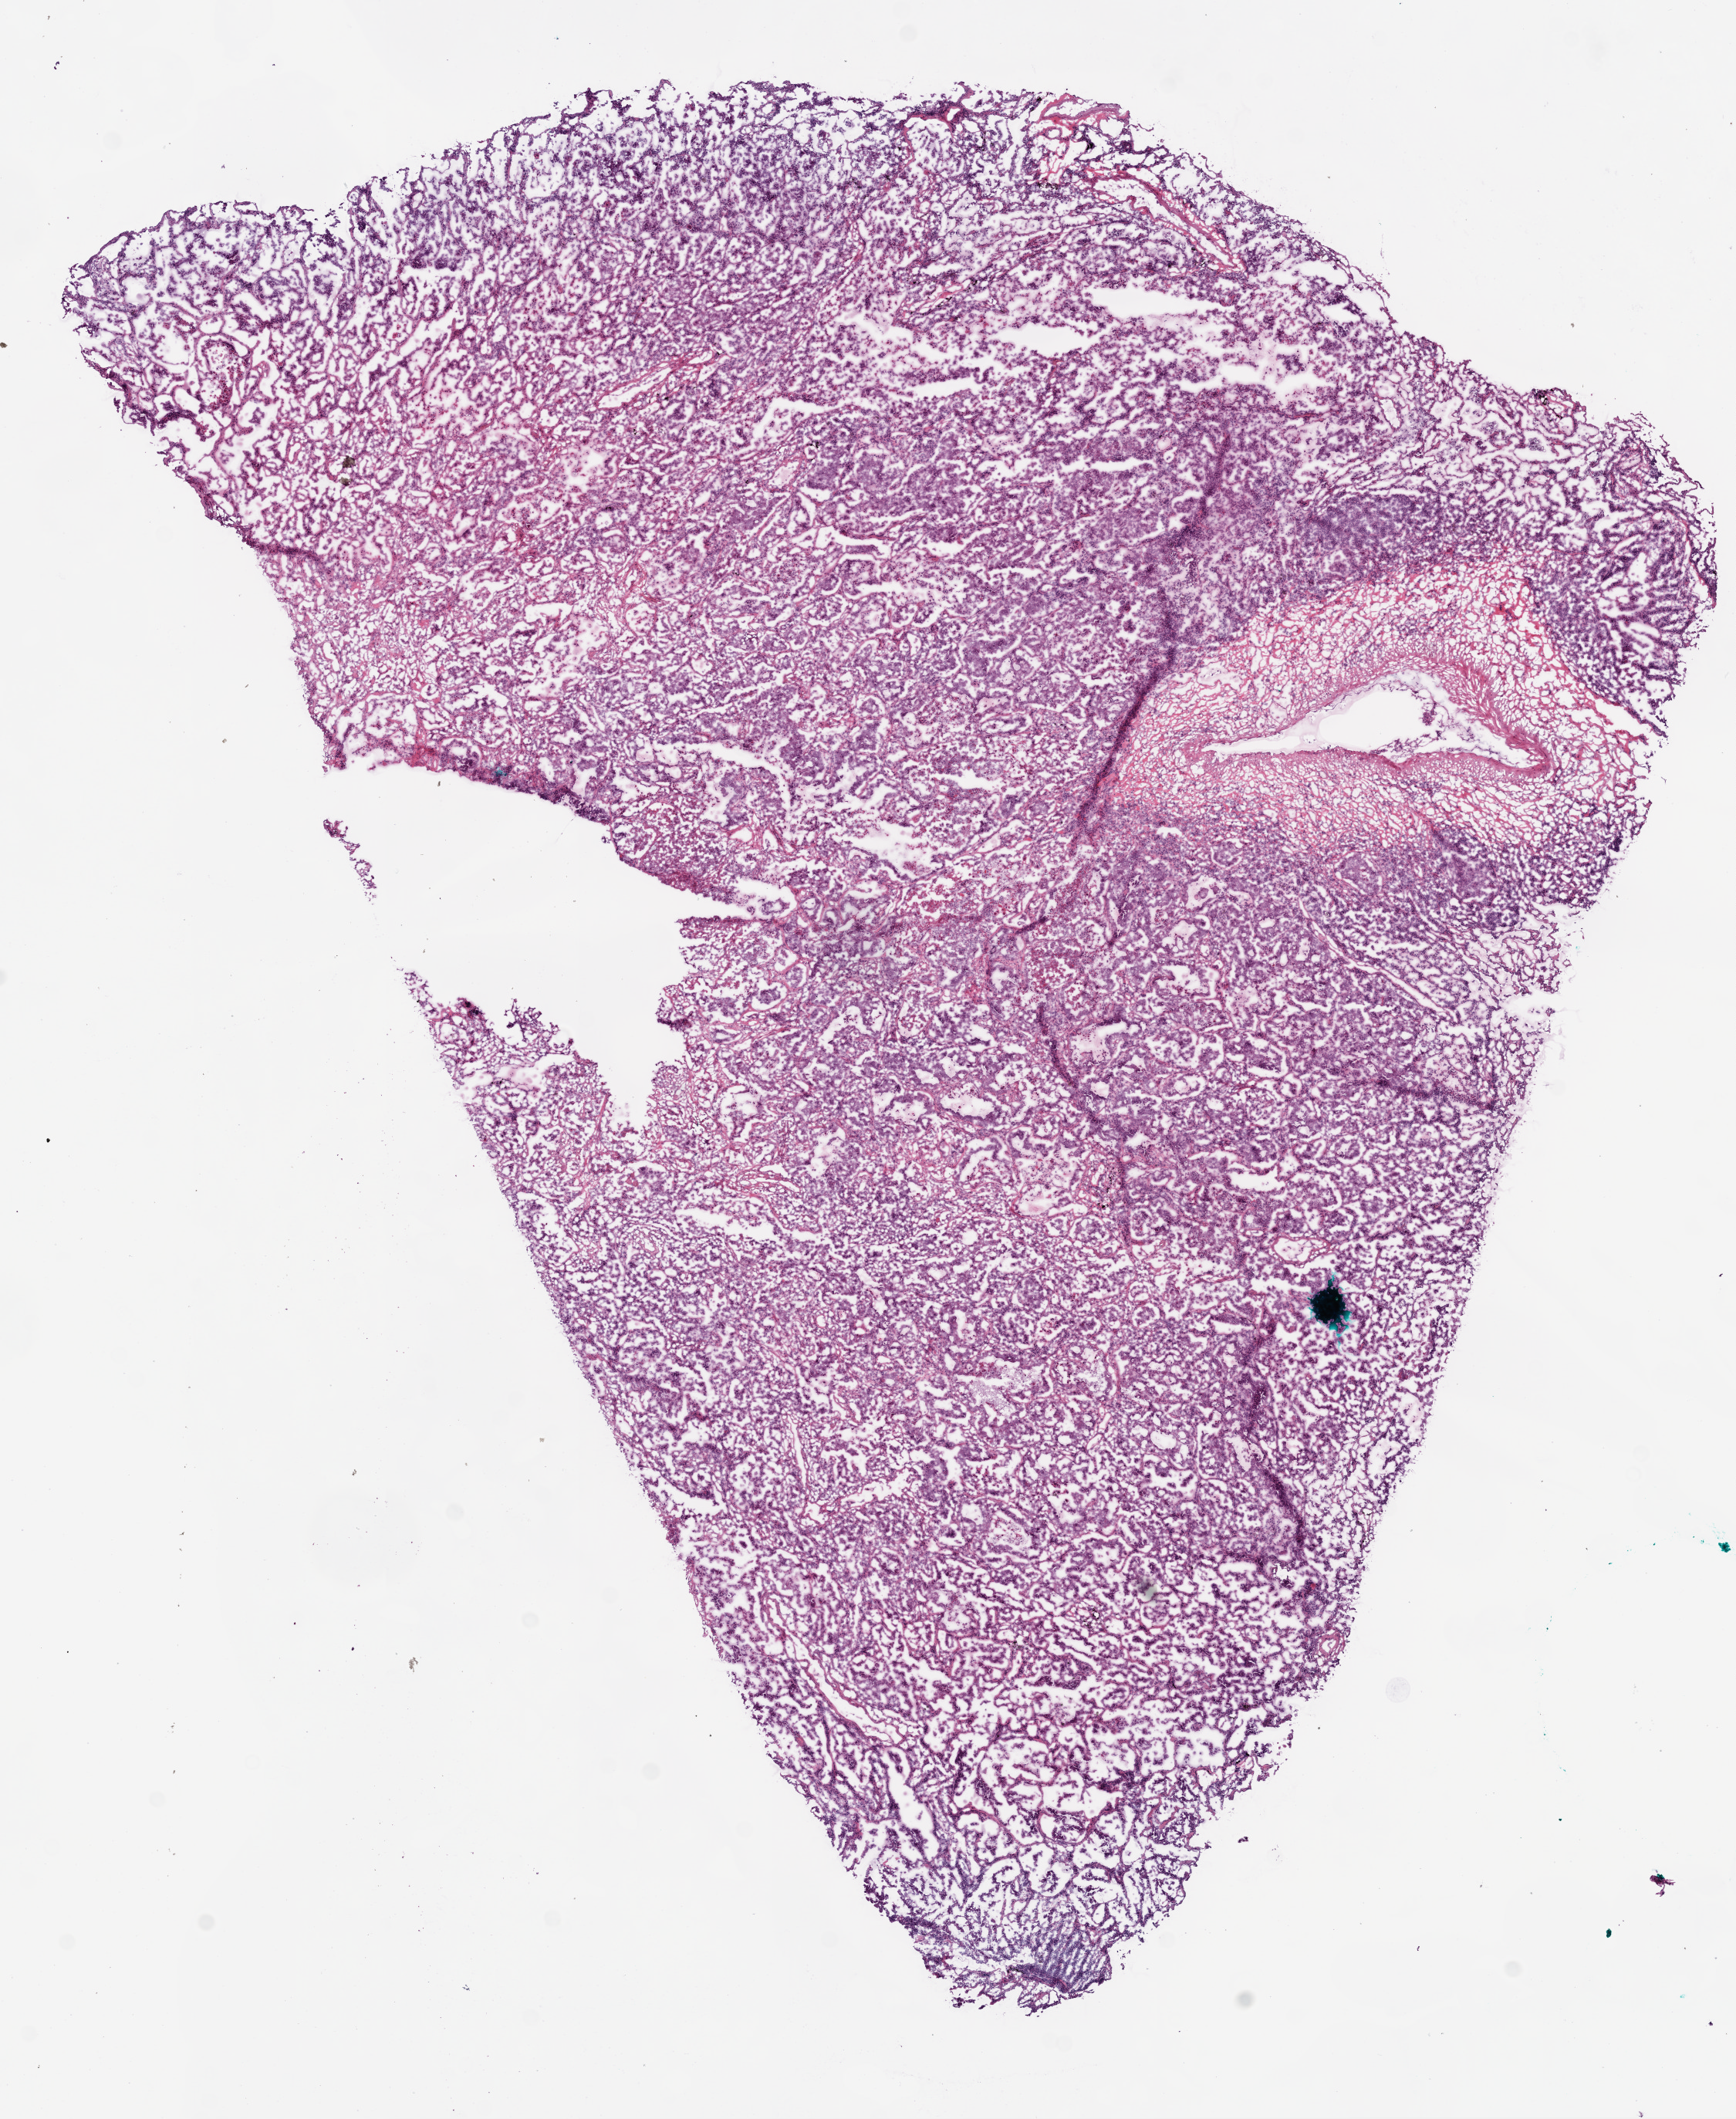
Digitized H&E tissue section (whole slide) — whole scanned area (about 9.0 x 11.0 mm, from a 20x scan) shown as a low-resolution overview; frozen section; lung, primary tumour sample. Patient: female, age at initial diagnosis 77 years. Composition of this section per pathologist review: tumour cells 88%, tumour nuclei 95%, normal cells 0%, stromal cells 10%, necrosis 2%.
Histologic diagnosis: Adenocarcinoma, NOS (upper lobe, lung). AJCC pathologic stage: IIIA.